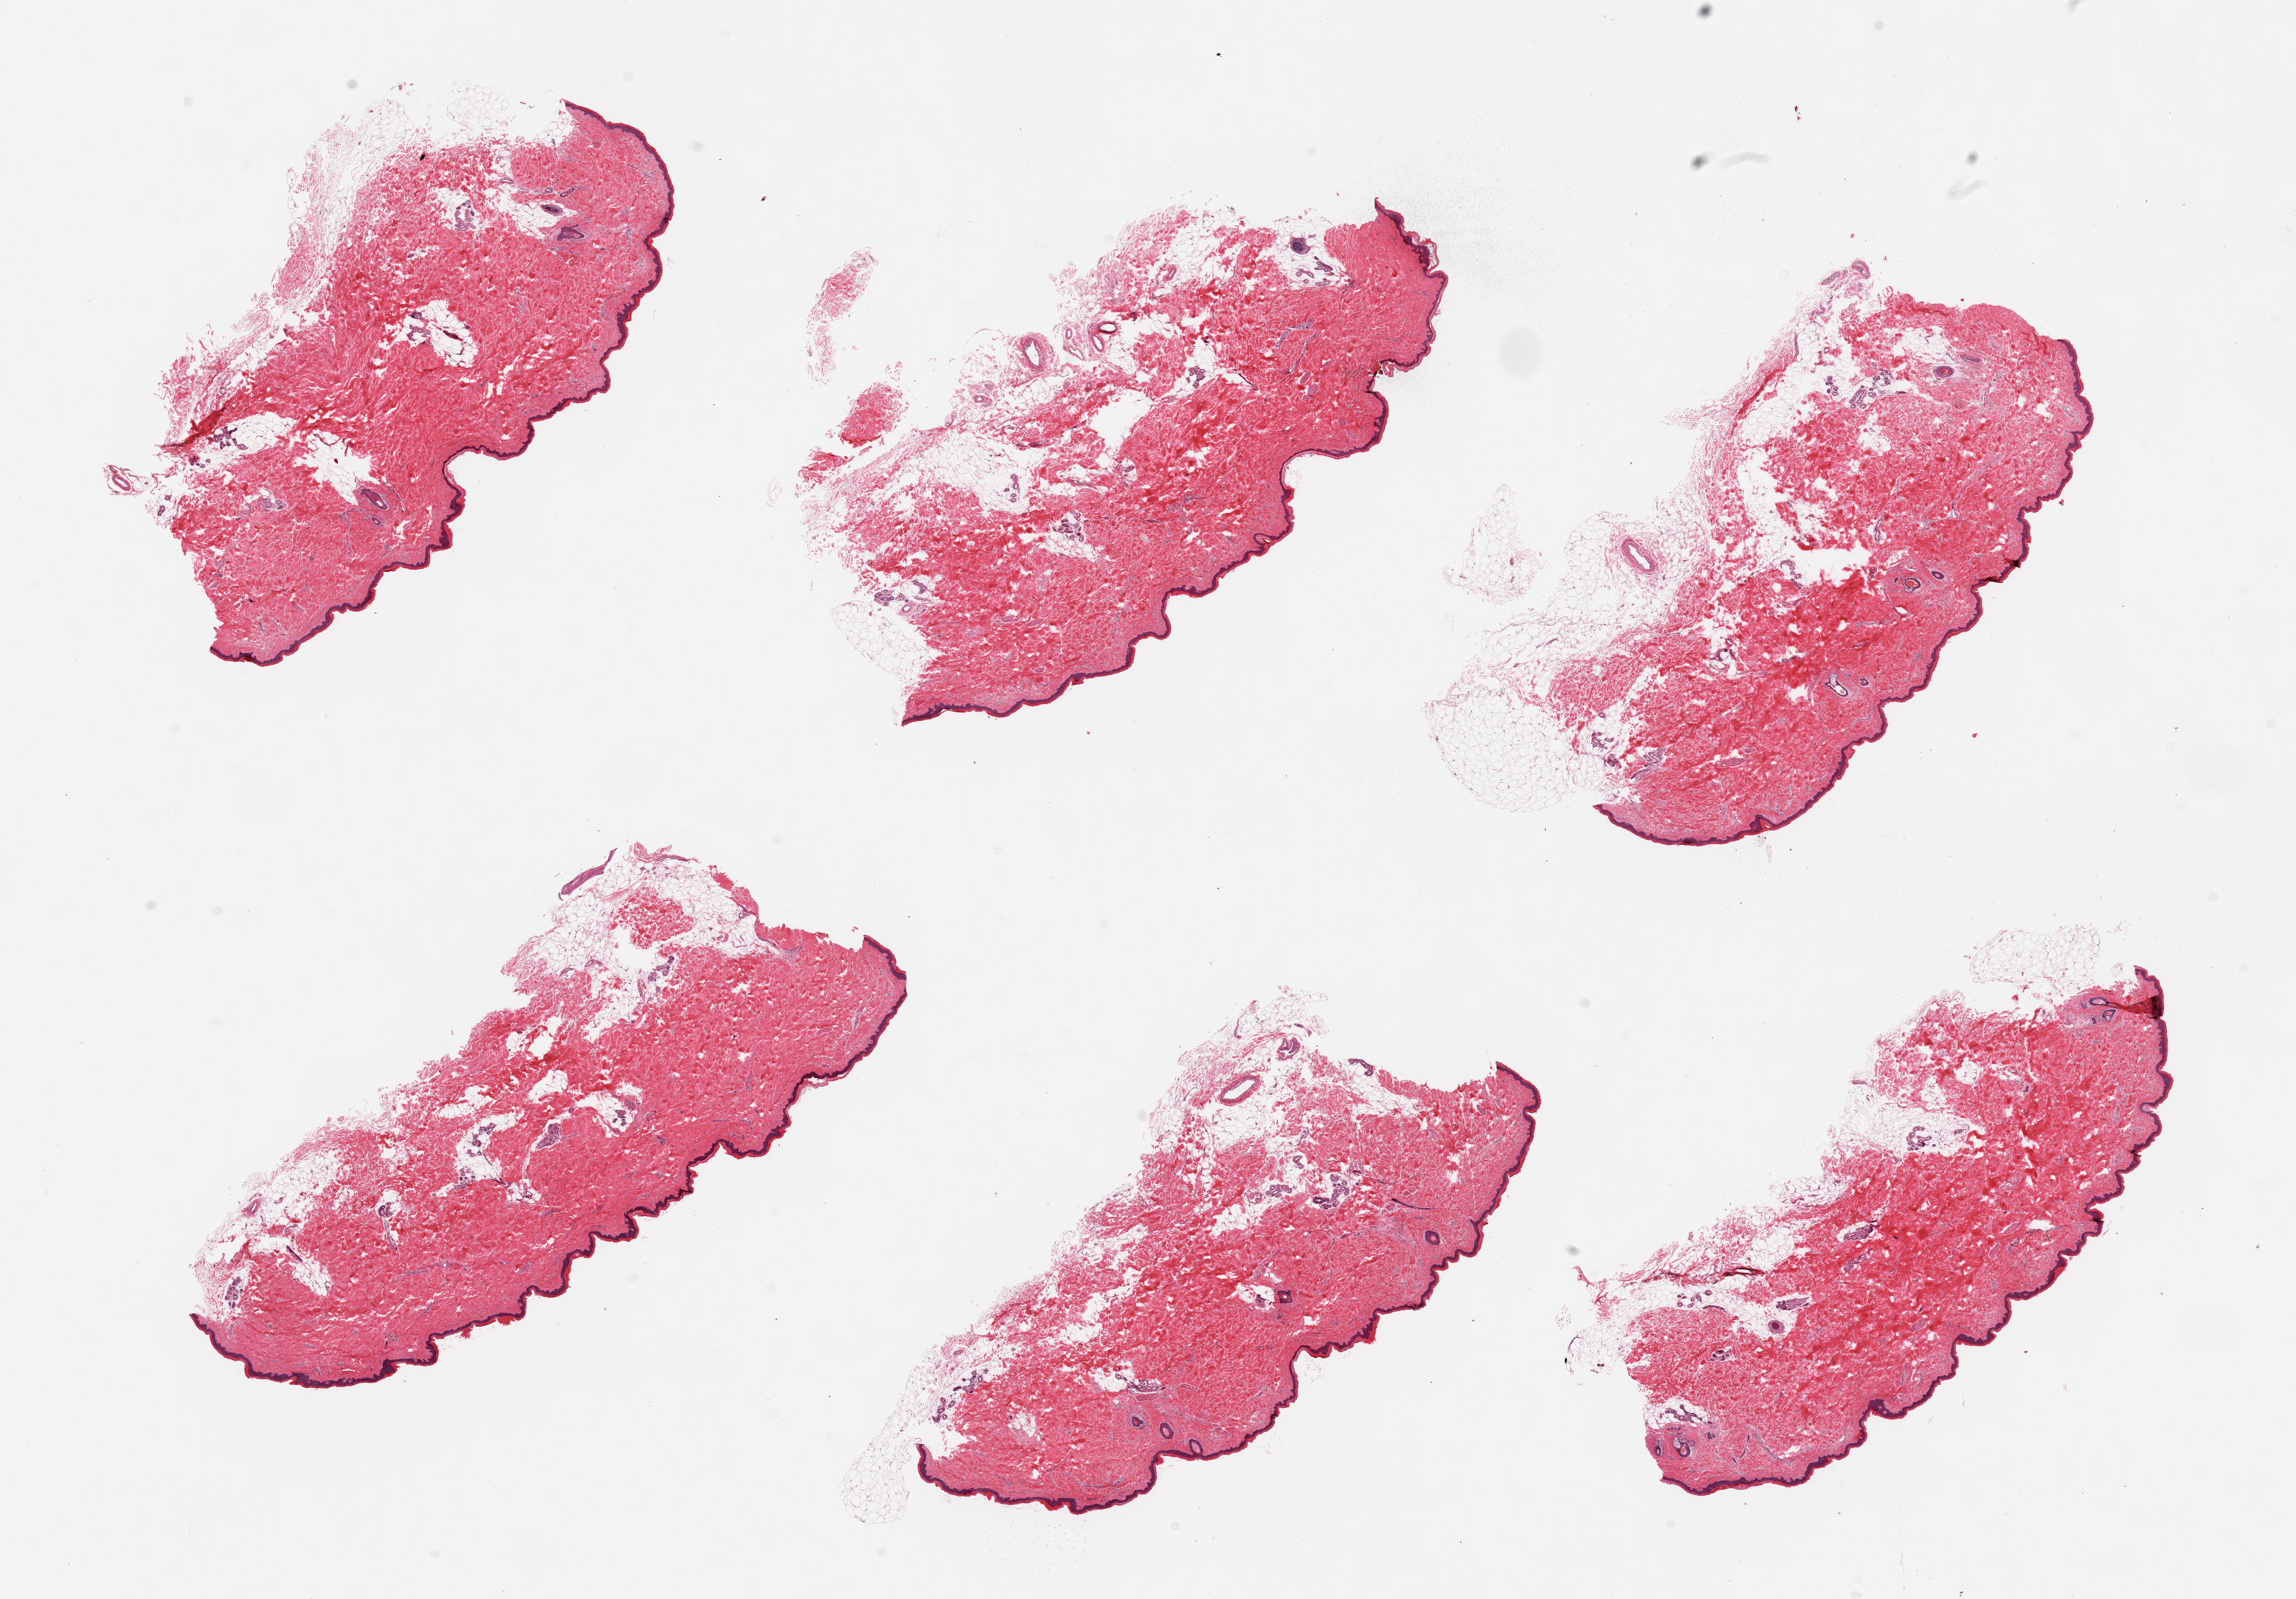
Digitized H&E-stained section, brightfield, shown as a low-resolution overview of the whole scanned area (about 24.6 x 17.1 mm, slide scanned at 20x). PAXgene-fixed paraffin-embedded (PFPE) section. Sampled site (target tissue): skin of lower leg. Donor tissue sample.
* reviewer comment on this tissue sample: 6 pieces; each with residual attached fat up to ~15%, epidermis is ~30 microns thick